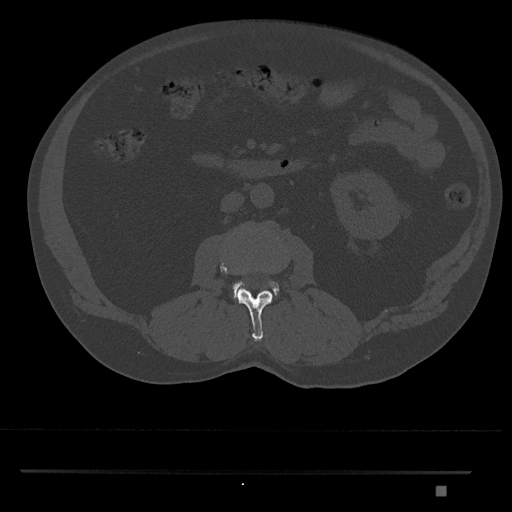
CT including the spine, one axial slice. Slice 725 of 1134 in the series (ordered by position). Bone window (W 1800 / L 400 HU). 0.5 mm slice thickness. 512 × 512 image matrix, field of view 429 × 429 mm. Patient: male, 65 years. Case-level facts recorded for this patient, not image findings: primary cancer: prostate.
Outlined on this slice (semi-automatic segmentation, software-assisted and operator-edited):
- L2 vertebra: bounding box <220,263,273,341> (left, top, right, bottom; pixels)
- L3 vertebra: <232,281,279,297>